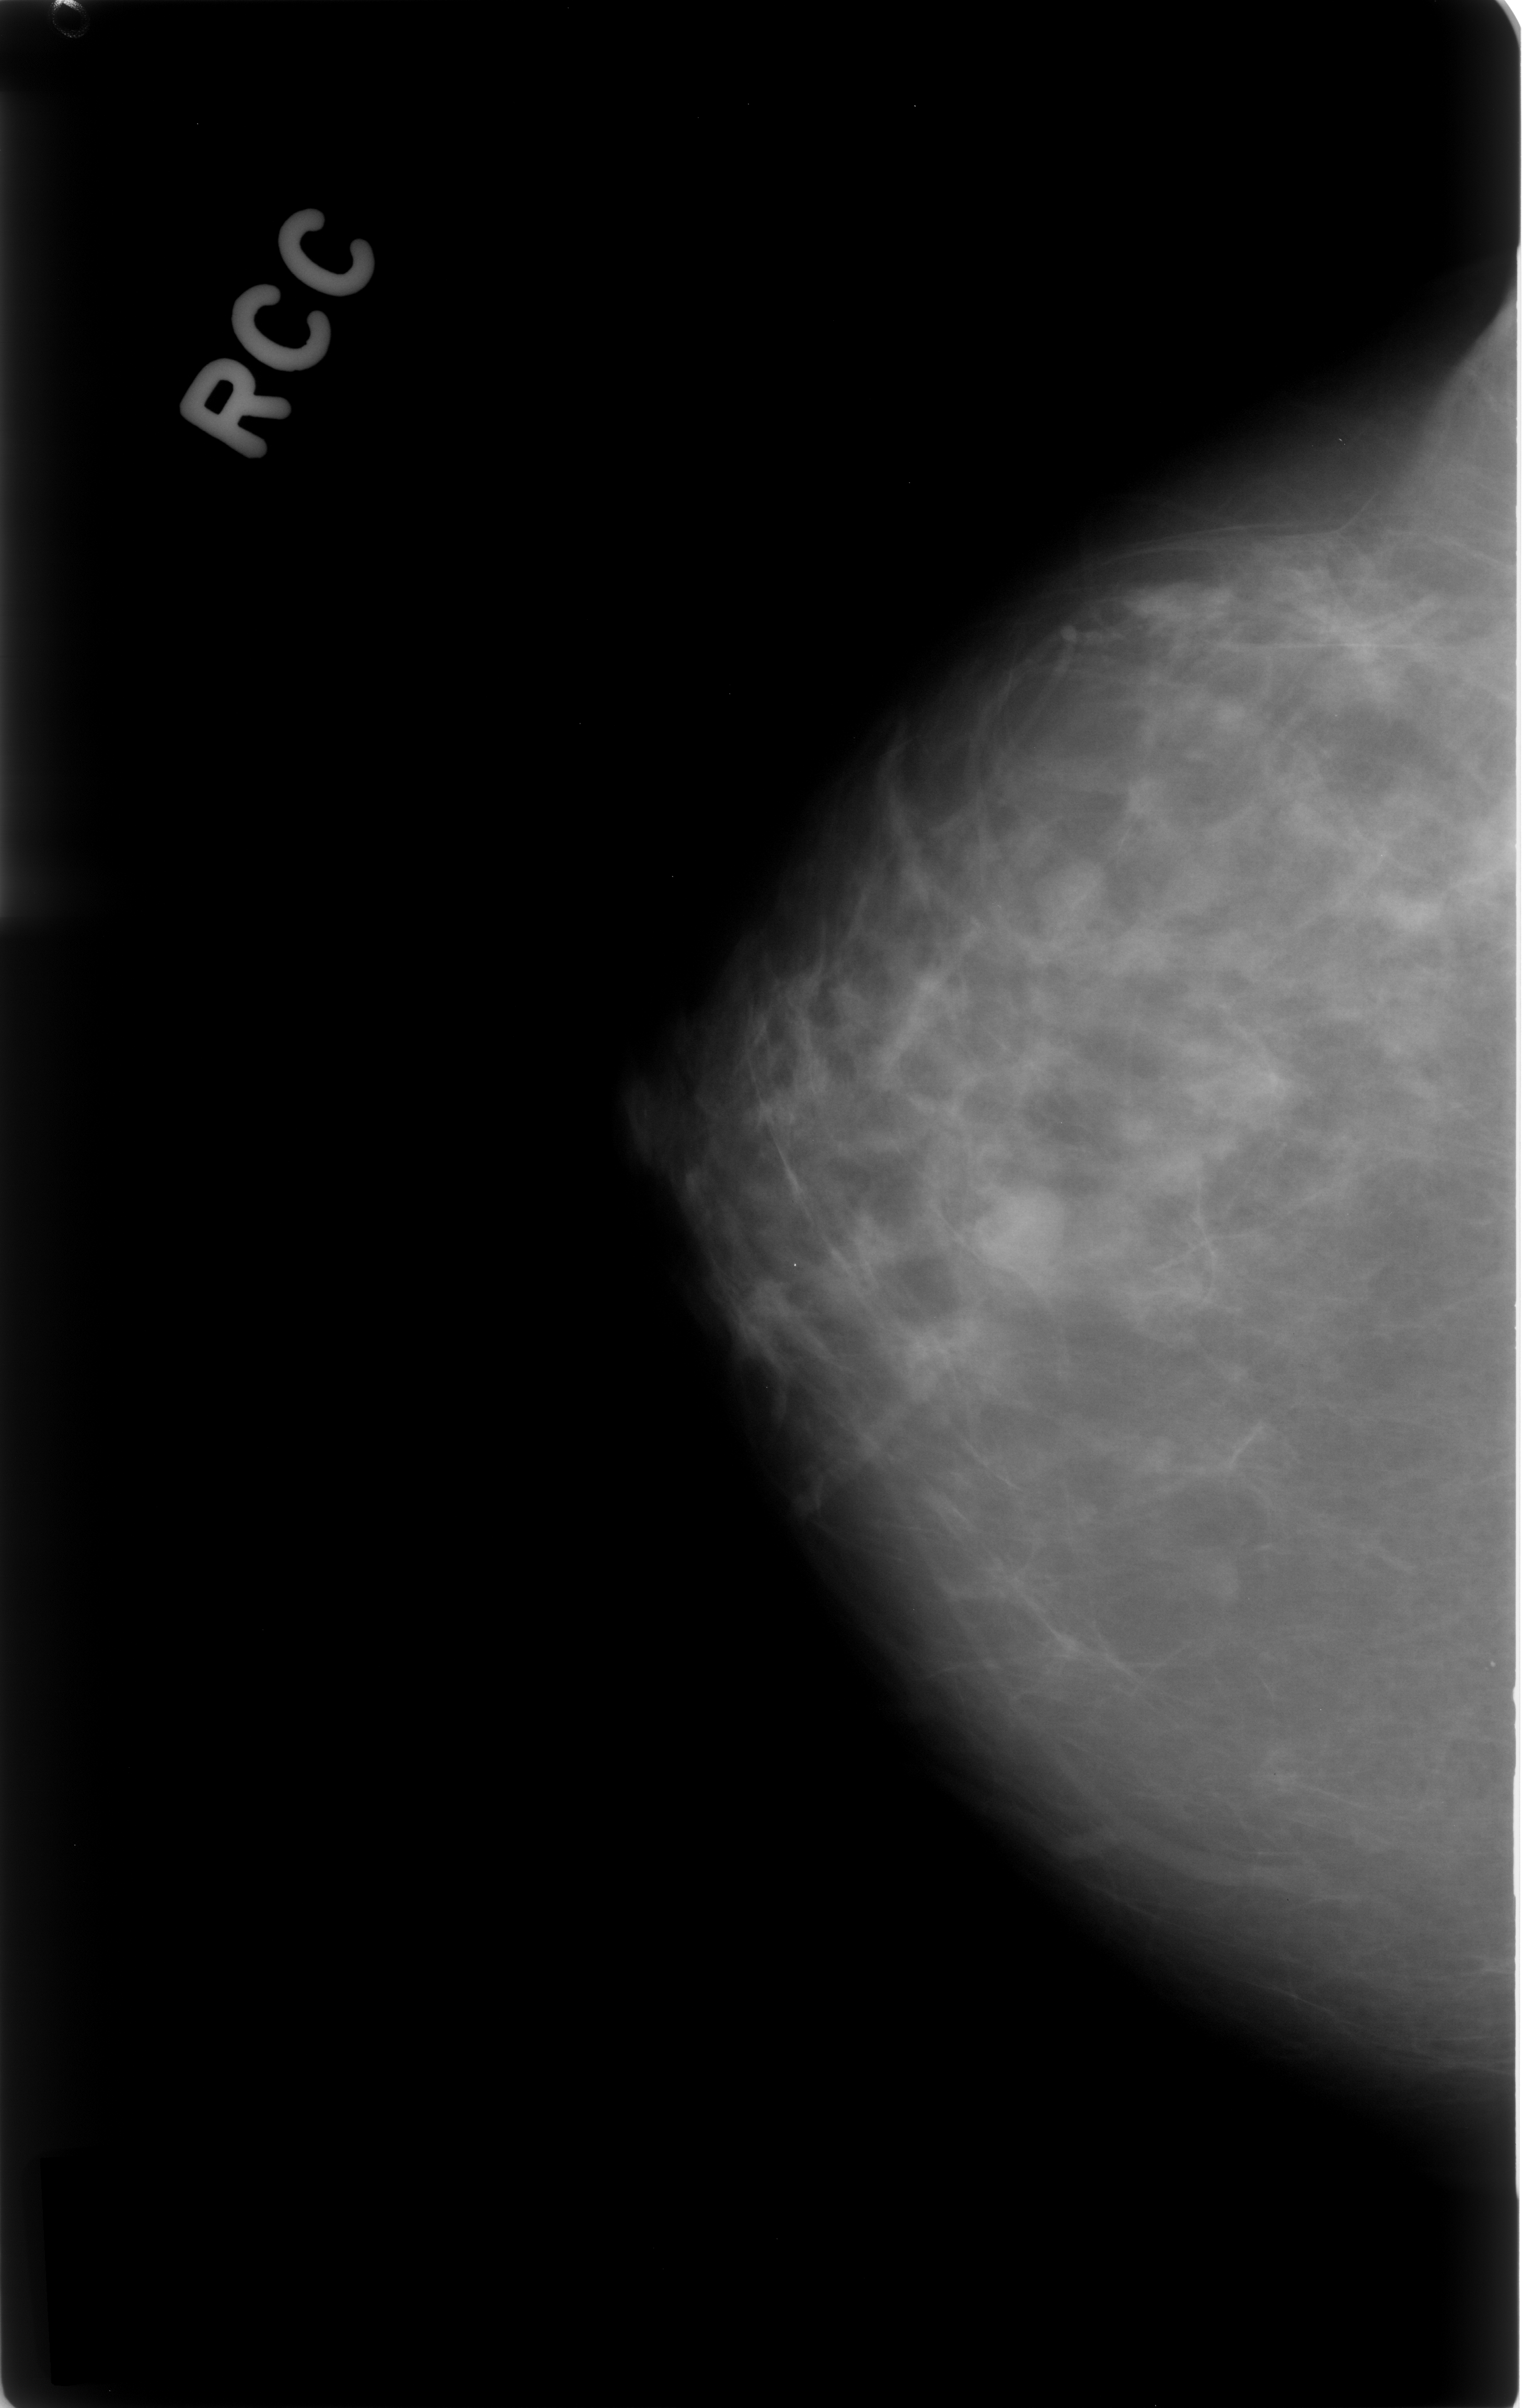
Digitized screen-film mammogram. Right breast. Craniocaudal (CC) view. Breast composition: scattered fibroglandular densities (BI-RADS density category 2 of 4). 1522 × 2408 image matrix.
Expert-marked regions of interest on this film, with their recorded descriptors:
- mass, shape oval, margins circumscribed; BI-RADS assessment category 3; pathology (as recorded): benign: bounding box [x1, y1, x2, y2] px = [950, 1180, 1069, 1306]